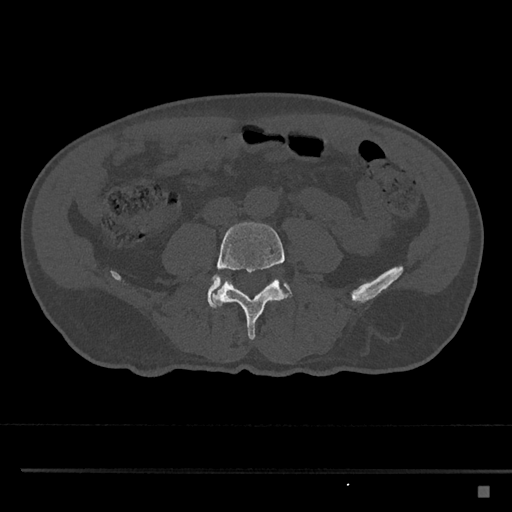
CT including the spine, one axial slice; slice 629 of 797 in the series (ordered by position); reconstruction kernel Br40s/3; 120 kVp; bone window (W 1800 / L 400 HU); 0.5 mm slice thickness; 512 × 512 image matrix. Patient: male, 59 years. Case-level facts recorded for this patient, not image findings: primary cancer: prostate.
Outlined on this slice (semi-automatic segmentation, software-assisted and operator-edited):
- L4 vertebra: bounding box [x1, y1, x2, y2] px = [212, 222, 290, 340]
- L5 vertebra: [207, 275, 293, 309]